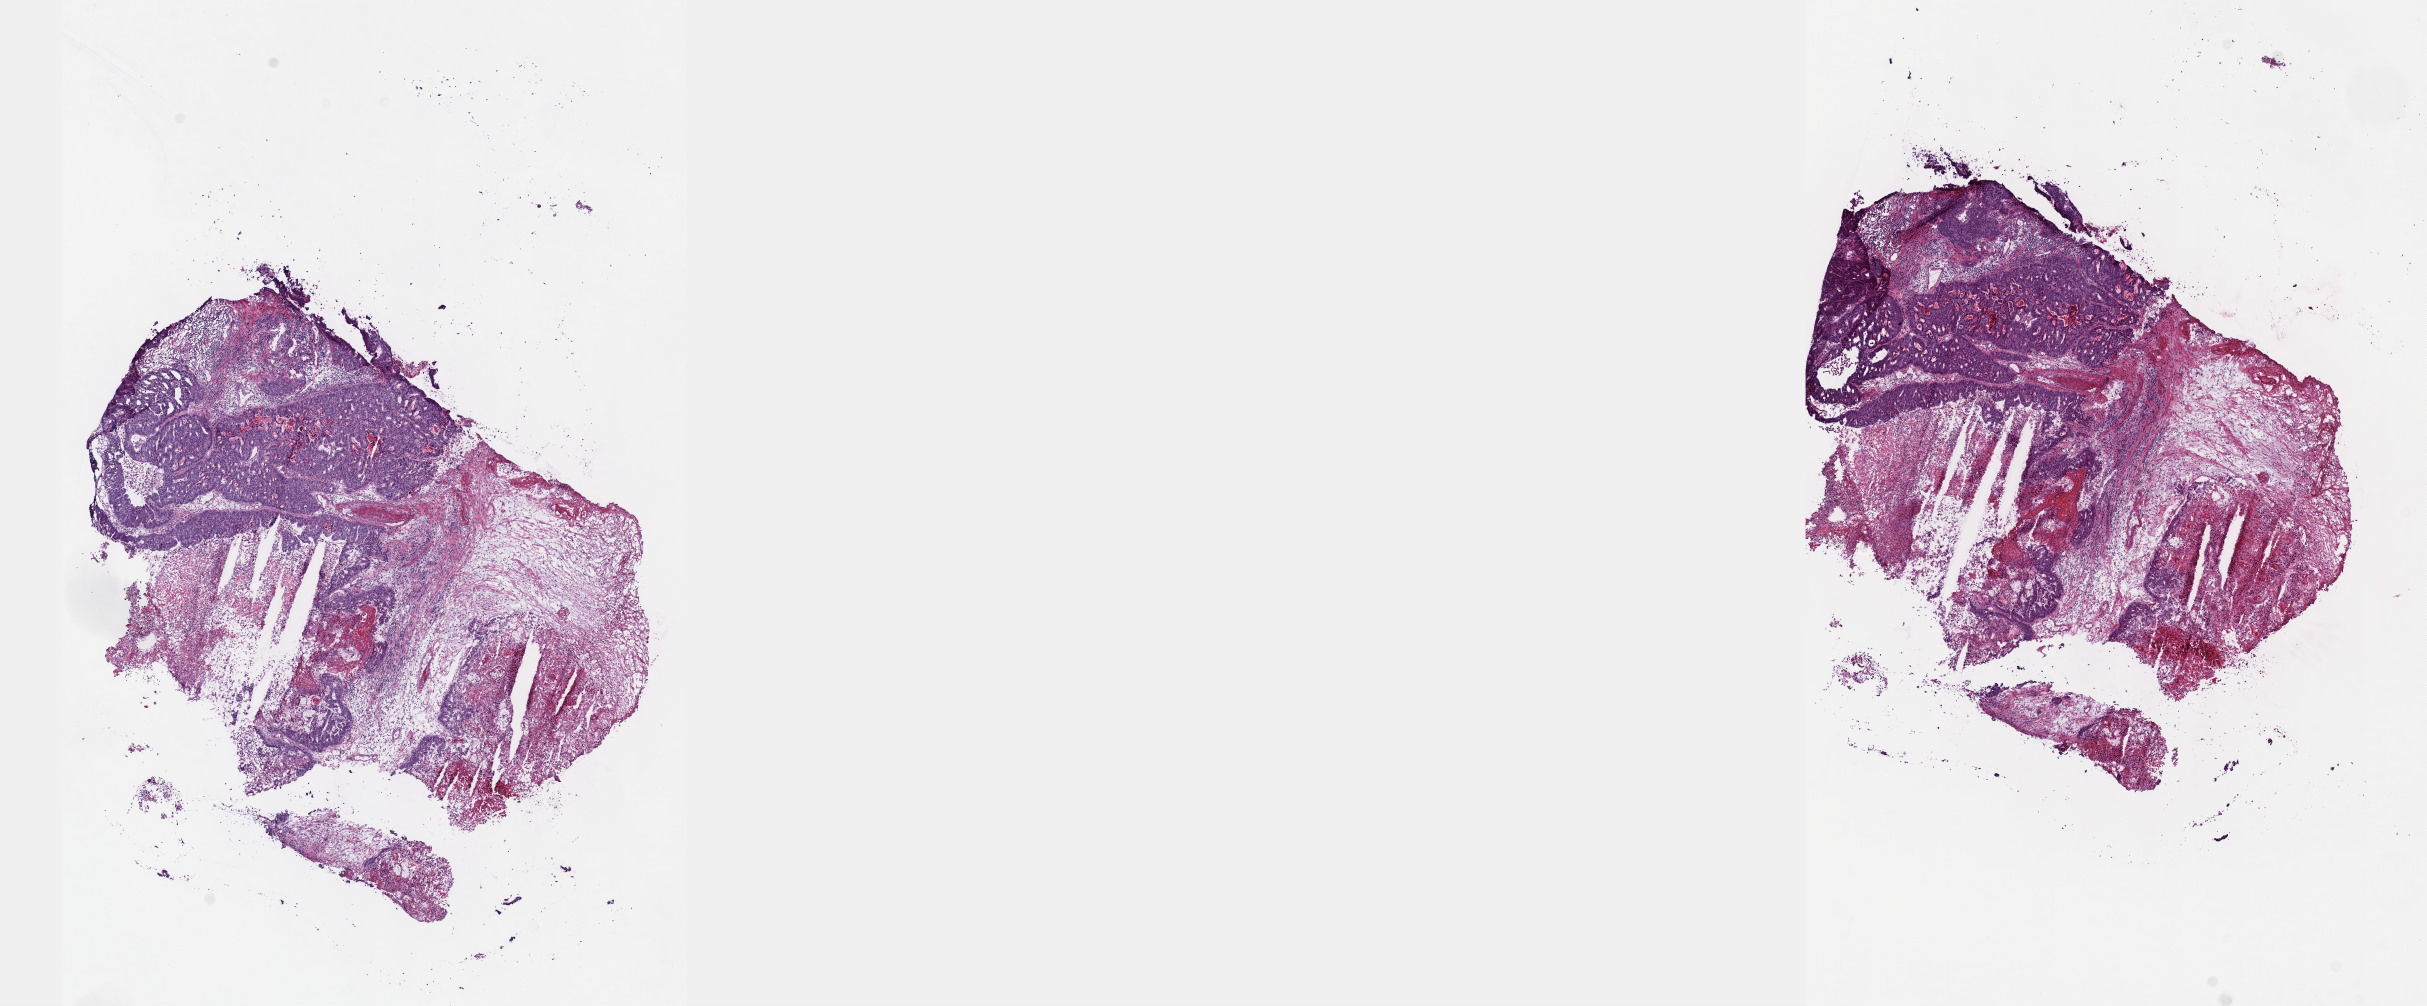
H&E whole-slide image — shown as a low-resolution overview of the whole scanned area (about 19.6 x 8.1 mm, from a 40x scan). Frozen section. Primary tumour sample from the cervix. Patient: female, age at initial diagnosis 63 years. Histologic grade: G2 (moderately differentiated). Pathologist review of this section (percent, as recorded): tumour cells 40%, tumour nuclei 60%, normal cells 40%, stromal cells 0%, necrosis 20%. Inflammatory infiltration, as recorded: lymphocyte infiltration 6%, monocyte infiltration 1%, neutrophil infiltration 5%.
• pathologic diagnosis: Mucinous adenocarcinoma, endocervical type
• FIGO stage: IVA